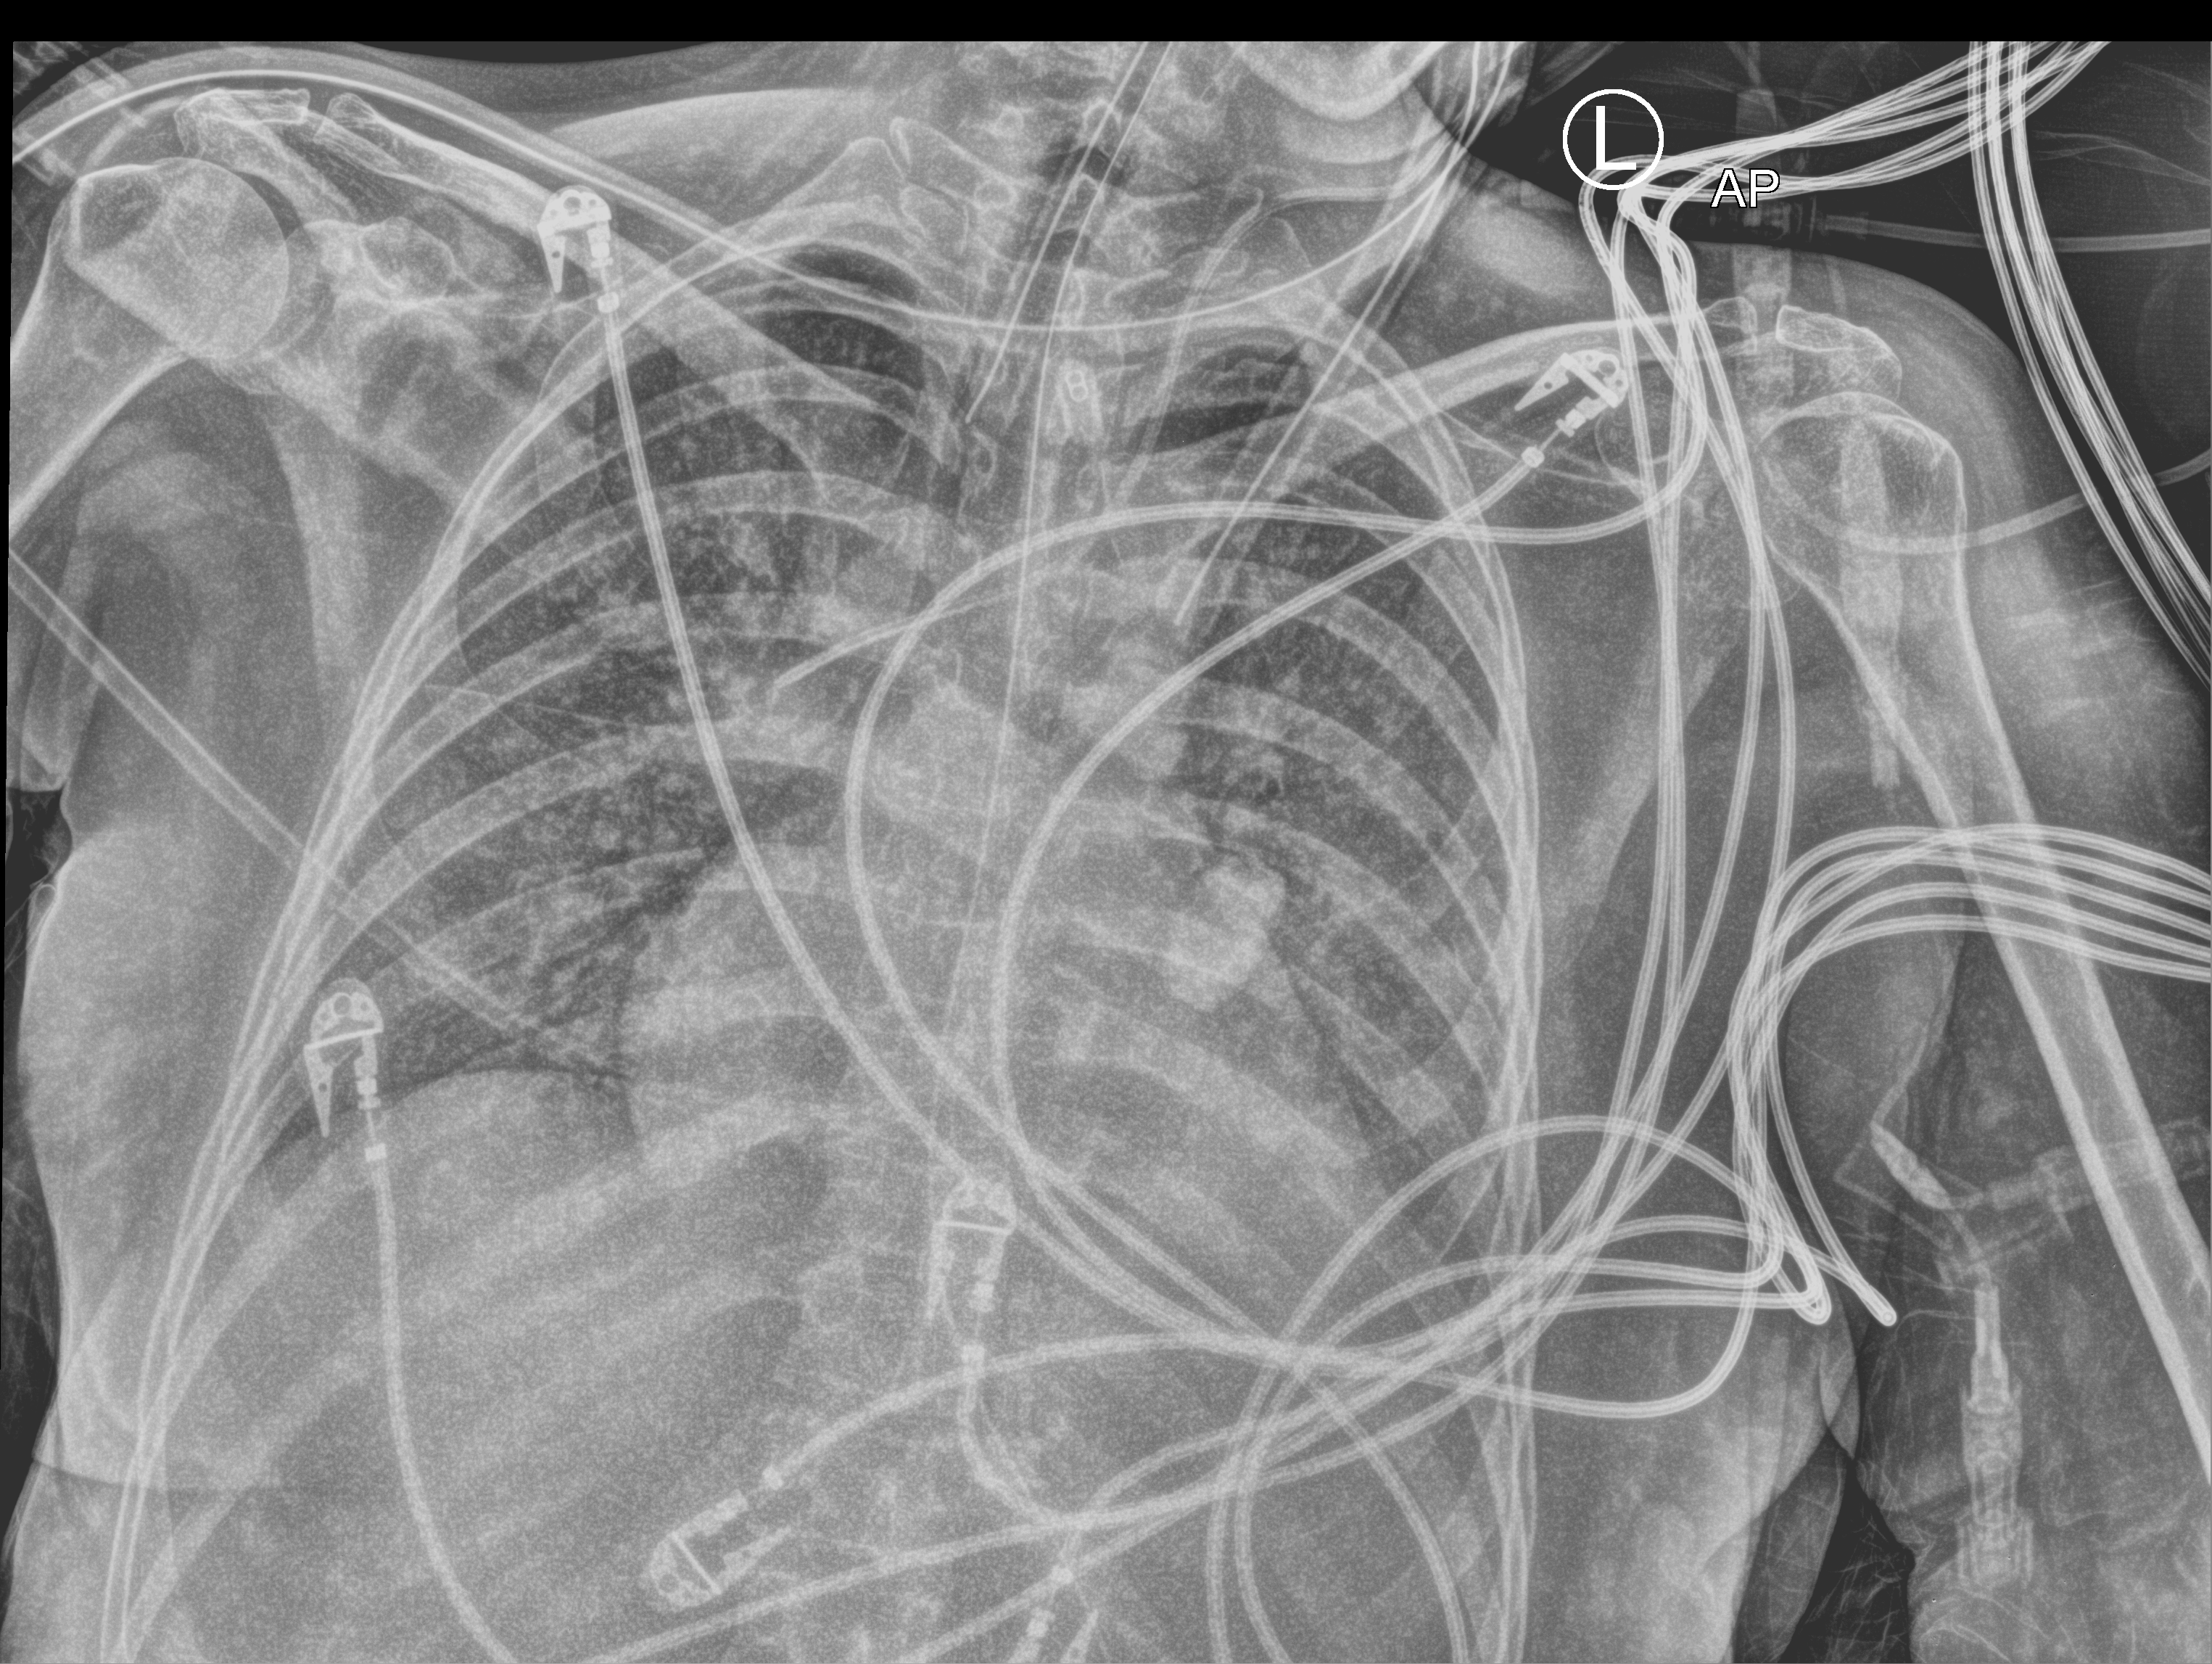
Bedside chest radiograph (computed radiography), anteroposterior (AP) projection. Patient hospitalised with COVID-19, aged 18–59 years.
Hospital-stay facts (about this admission, not read from this image; timing relative to this image not recorded): admitted to intensive care during this hospital stay: yes; mechanically ventilated during this hospital stay: yes.